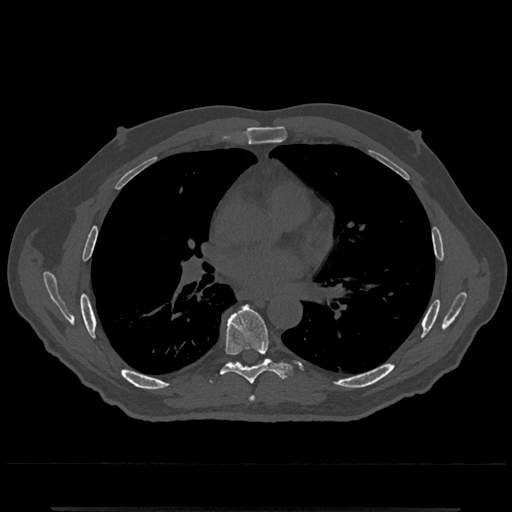
CT including the spine, one axial slice. Position 720 of 797 along the scan axis. Reconstruction kernel Br40s/3. Bone window (W 1800 / L 400 HU). 512 × 512 image matrix. Male patient, age 67 years. Case-level facts recorded for this patient, not image findings: primary cancer: prostate.
Structures marked on this image (semi-automatically segmented with operator editing):
- T6 vertebra: bounding box [x1, y1, x2, y2] px = [249, 396, 256, 402]
- T7 vertebra: [220, 305, 290, 385]